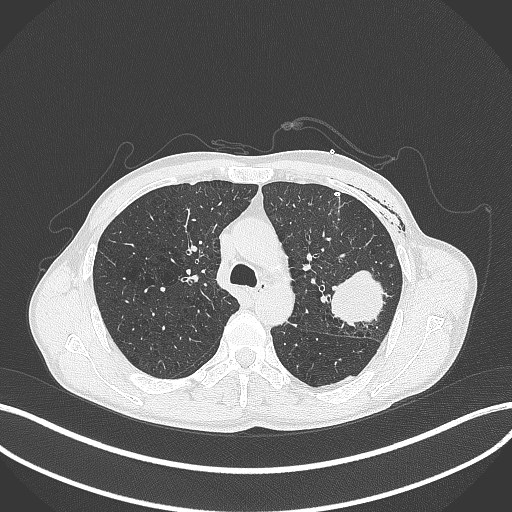
Chest CT, one axial slice; position 278 of 457 along the scan axis; reconstruction kernel B70f; 120 kVp; lung window (W 1500 / L -600 HU); 1 mm slice thickness; 512 × 512 image matrix, field of view 400 × 400 mm. Patient: male, 58 years. From the clinical record (not read from this slice): clinical TNM (as recorded): T3 N0 M0.
Annotated regions visible in this slice (rectangle marked by the reading radiologist):
- lung tumour (recorded histology: adenocarcinoma): bounding box (x1, y1, x2, y2) in pixels: (329, 268, 386, 328)